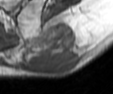
MRI of an extremity soft-tissue mass, one axial slice. Position 19 of 42 along the scan axis. MR volume resampled by the dataset authors to the PET/CT grid (not the native acquisition matrix). 3.27 mm slice thickness. 113 × 94 image matrix, field of view 110 × 92 mm. Male patient. Case-level facts recorded for this patient, not image findings: histological type: leiomyosarcoma; grade: intermediate; site of the primary tumour: left pelvis.
Annotated regions visible in this slice (expert contour drawn on MRI and transferred to this co-registered scan by the dataset authors):
- gross tumour volume (mass): bounding box [x1, y1, x2, y2] px = [26, 21, 82, 74]